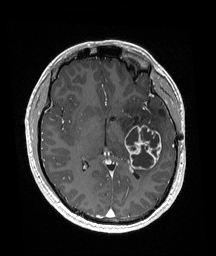
Brain MRI from a brain-tumour surgery series, one axial slice. T1-weighted post-contrast. 1 mm slice thickness. 216 × 256 image matrix. Case-level facts recorded for this patient, not image findings: histopathology: Glioneuronal tumor; WHO grade: 2; tumour location: Left Superior Temporal Gyrus.
Annotated regions visible in this slice (manually delineated by an expert):
- previous resection cavity: box from (x=161, y=111) to (x=165, y=115) px
- tumour: (x=125, y=125)–(x=162, y=170)